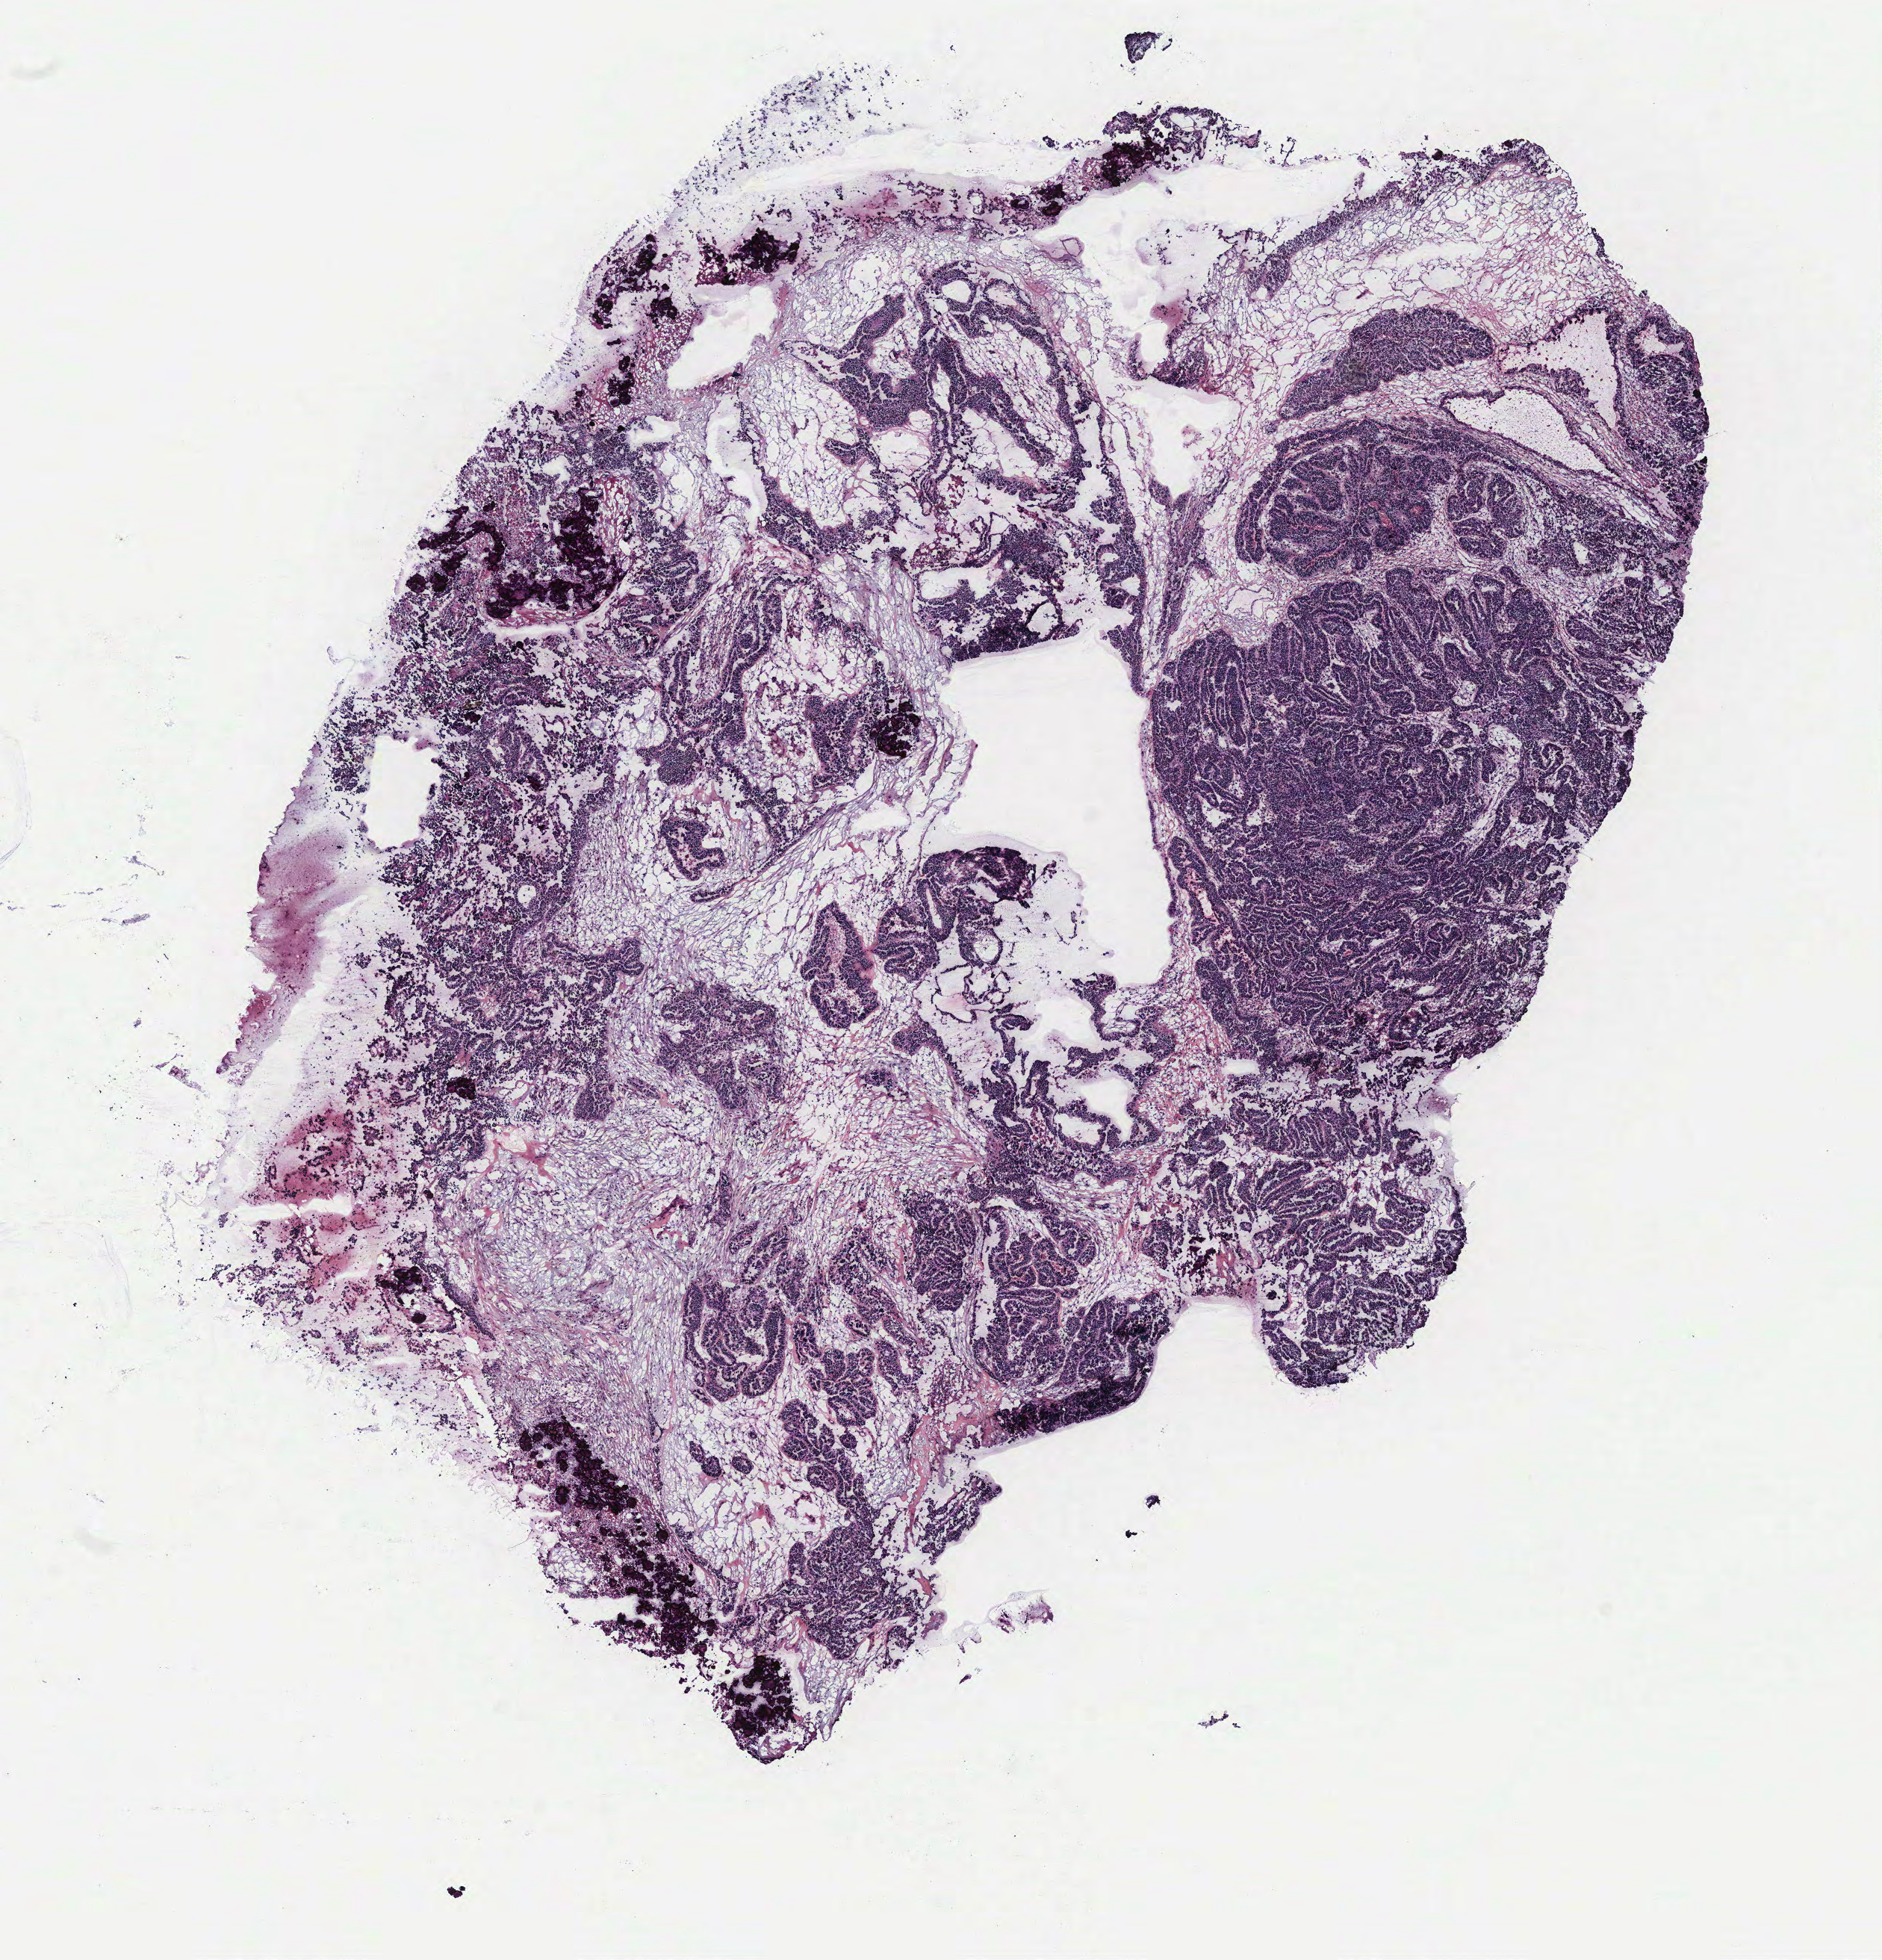
Digitized H&E tissue section (whole slide) — low-resolution overview of the scanned area, about 10.1 x 10.5 mm (slide scanned at 40x), tumour tissue sample, ovary. 57-year-old female patient.
Primary tumour site (as recorded): ovary. Histologic diagnosis: Serous adenocarcinoma, NOS.